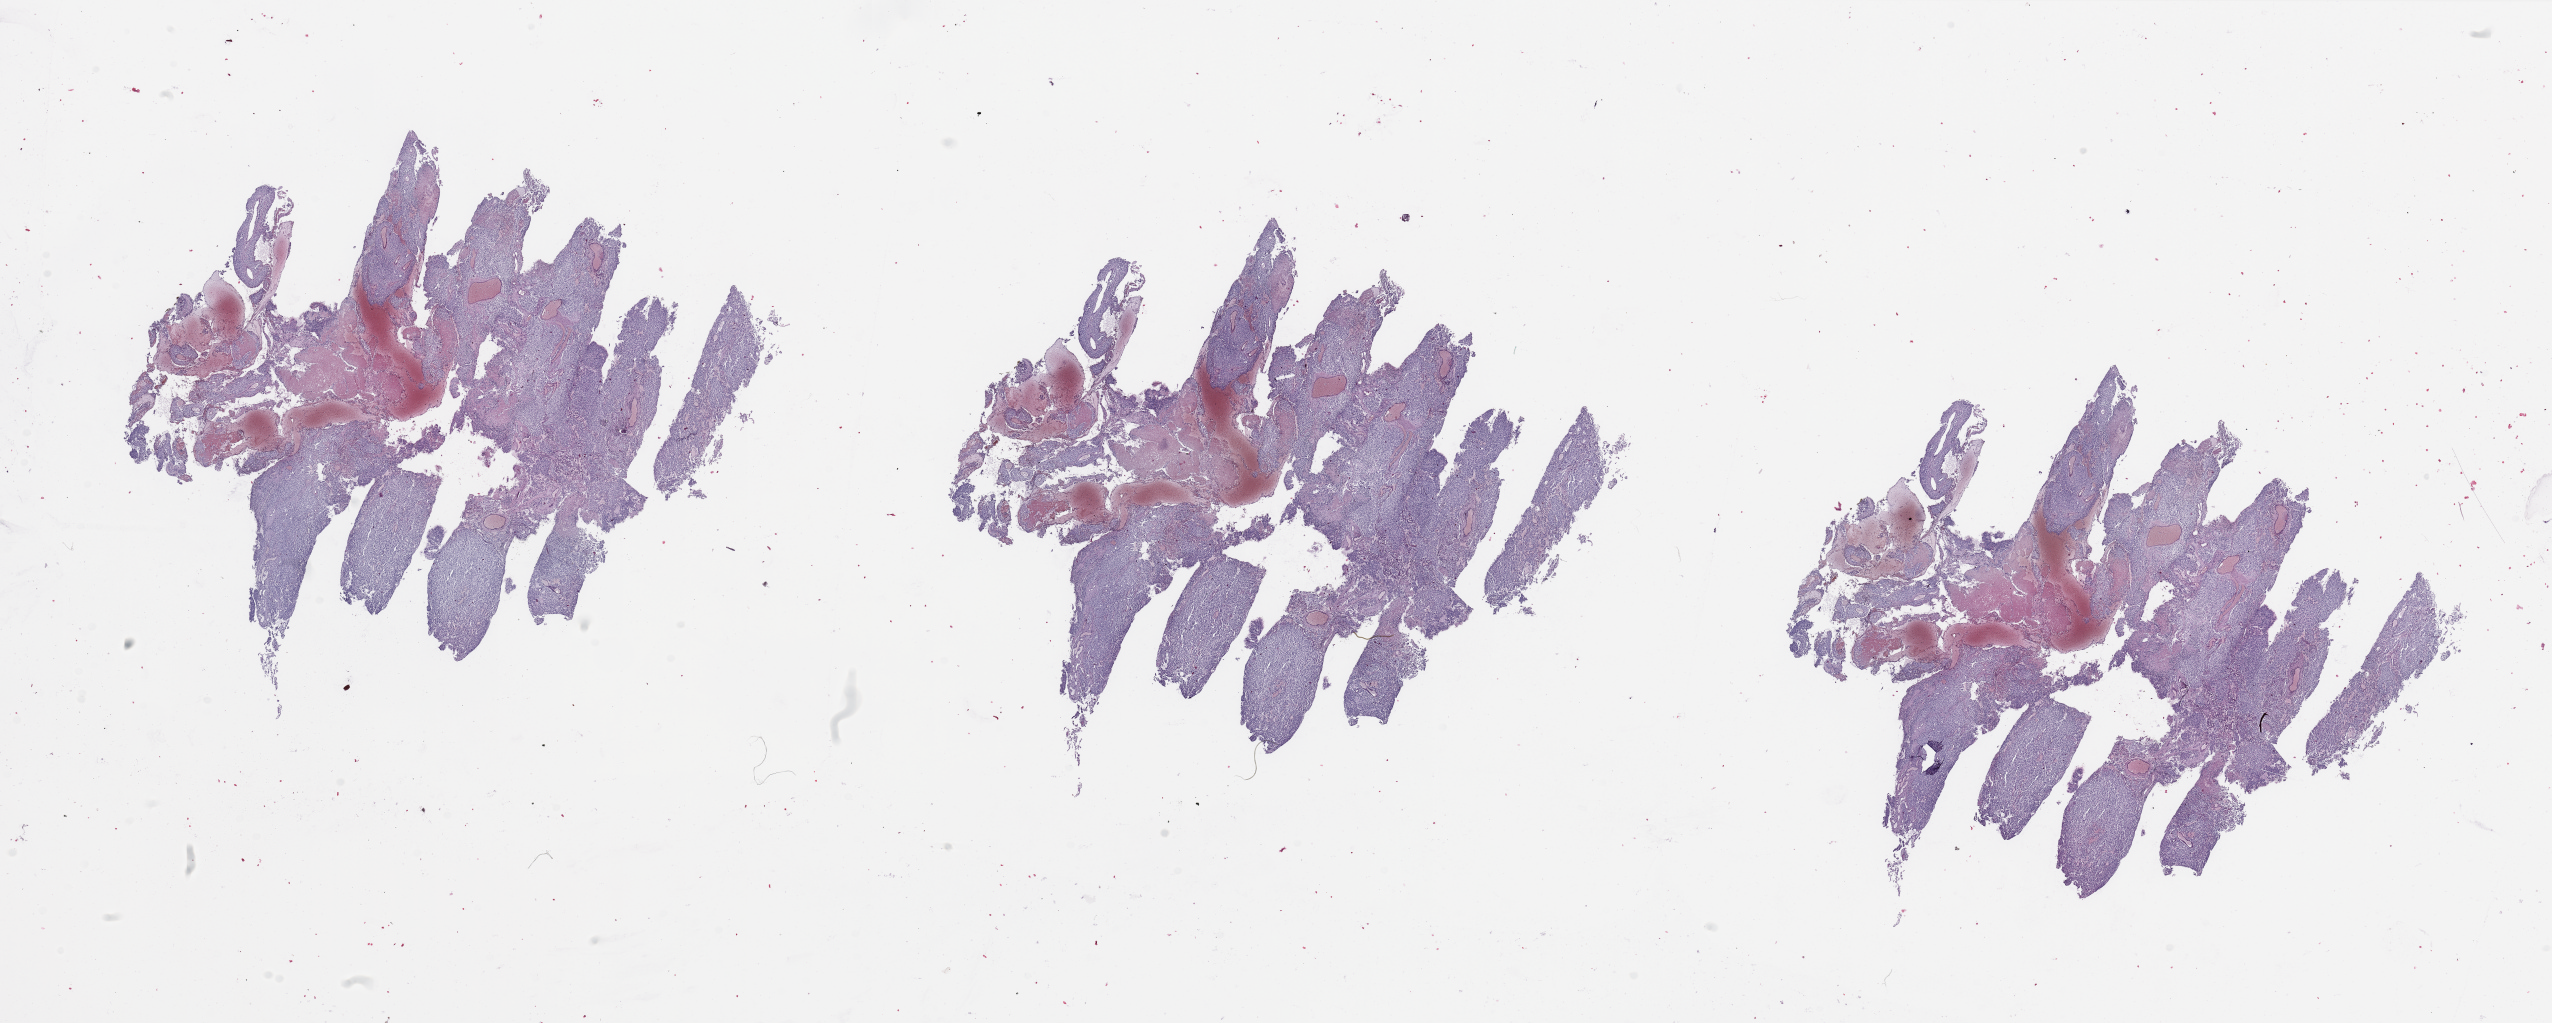
Whole-slide histology image, Hematoxylin and eosin (H&E) stained, a low-resolution overview of the entire scanned area, about 40.4 x 16.2 mm (slide scanned at 20x); tumour tissue sample, brain. 40-year-old male patient.
• primary tumour site (as recorded): parietal lobe
• histologic diagnosis: Glioblastoma